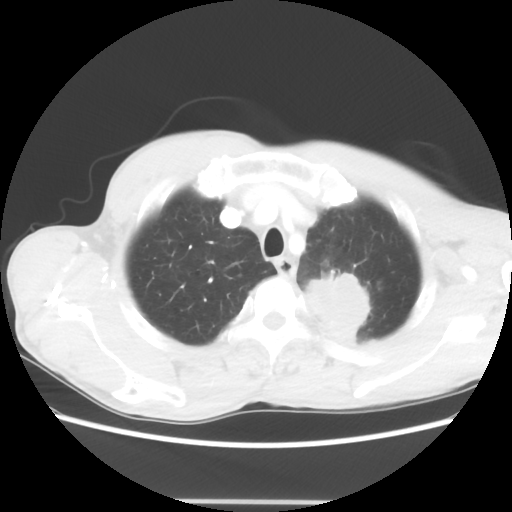
Chest CT, one axial slice; position 55 of 62 along the scan axis; 100 kVp; lung window (W 1500 / L -600 HU); 5 mm slice thickness; 512 × 512 image matrix, field of view 360 × 360 mm. Patient: male, 61 years. Case-level facts recorded for this patient, not image findings: clinical TNM (as recorded): T3 N1 M1.
Outlined on this slice (rectangle marked by the reading radiologist):
- lung tumour (recorded histology: adenocarcinoma): bounding box [x1, y1, x2, y2] px = [304, 265, 371, 353]